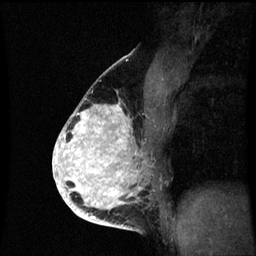
Breast MRI (dynamic contrast-enhanced), one sagittal slice. Position 37 of 60 along the scan axis. Dynamic contrast-enhanced series, image 2 of 3 at this slice position (ordered by acquisition). 1.5 T. TE 4.2 ms, TR 8.9 ms. 256 × 256 image matrix, field of view 200 × 200 mm. Female patient, age 35 years. From the clinical record (not read from this slice): setting: breast cancer imaged before/during neoadjuvant chemotherapy; receptor status: HR-positive, HER2-negative.
Structures marked on this image (semi-automatically segmented with operator editing):
- analysis volume of interest (the breast-tissue region the enhancement analysis was run in; not a lesion): box from (x=66, y=98) to (x=155, y=215) px
- tumour enhancement mask (voxels above the 70 % enhancement threshold inside the analysis volume of interest): (x=66, y=104)–(x=131, y=215)